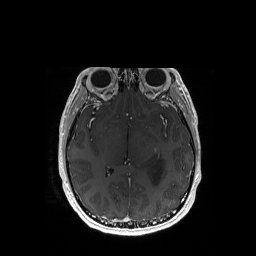
Brain MRI from a brain-tumour surgery series, one axial slice; slice 93 of 192 in the series (ordered by position); T1-weighted post-contrast; 256 × 256 image matrix, field of view 256 × 256 mm. Case-level facts recorded for this patient, not image findings: histopathology: Astrocytoma; WHO grade: 3; IDH mutation: yes.
Annotated regions visible in this slice (manually delineated by an expert):
- tumour: bounding box <149,150,163,185> (left, top, right, bottom; pixels)